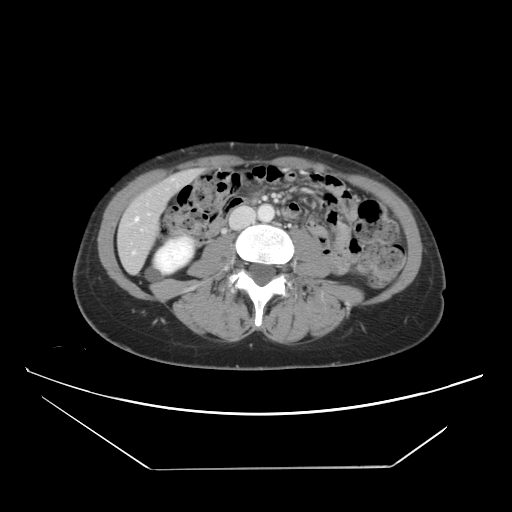
Contrast-enhanced abdominal CT, one axial slice; position 11 of 42 along the scan axis; intravenous contrast given; soft-tissue window (W 400 / L 40 HU); 5 mm slice thickness; 512 × 512 image matrix, field of view 399 × 399 mm. Female patient, age 52 years. From the clinical record (not read from this slice): diagnosis: colorectal cancer liver metastases, imaged before liver resection; multiple liver metastases: yes; largest metastasis: 5.5 cm; chemotherapy before resection: yes.
Structures marked on this image (expert manual segmentation):
- hepatic veins: box from (x=127, y=178) to (x=179, y=226) px
- liver: (x=120, y=171)–(x=197, y=271)
- planned liver remnant (the part of the liver to remain after resection): (x=129, y=171)–(x=195, y=219)
- portal vein (with intrahepatic branches): (x=264, y=197)–(x=266, y=199)